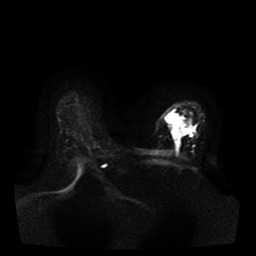
Breast MRI, one axial slice; position 30 of 41 along the scan axis; diffusion-weighted series; image 2 of 4 stored at this slice position (different b-values; order by instance number); 1.5 T; 5 mm slice thickness; 256 × 256 image matrix, field of view 330 × 330 mm. Female patient.
Structures marked on this image (manually delineated by an expert):
- tumour on diffusion-weighted imaging: bounding box <167,114,189,148> (left, top, right, bottom; pixels)